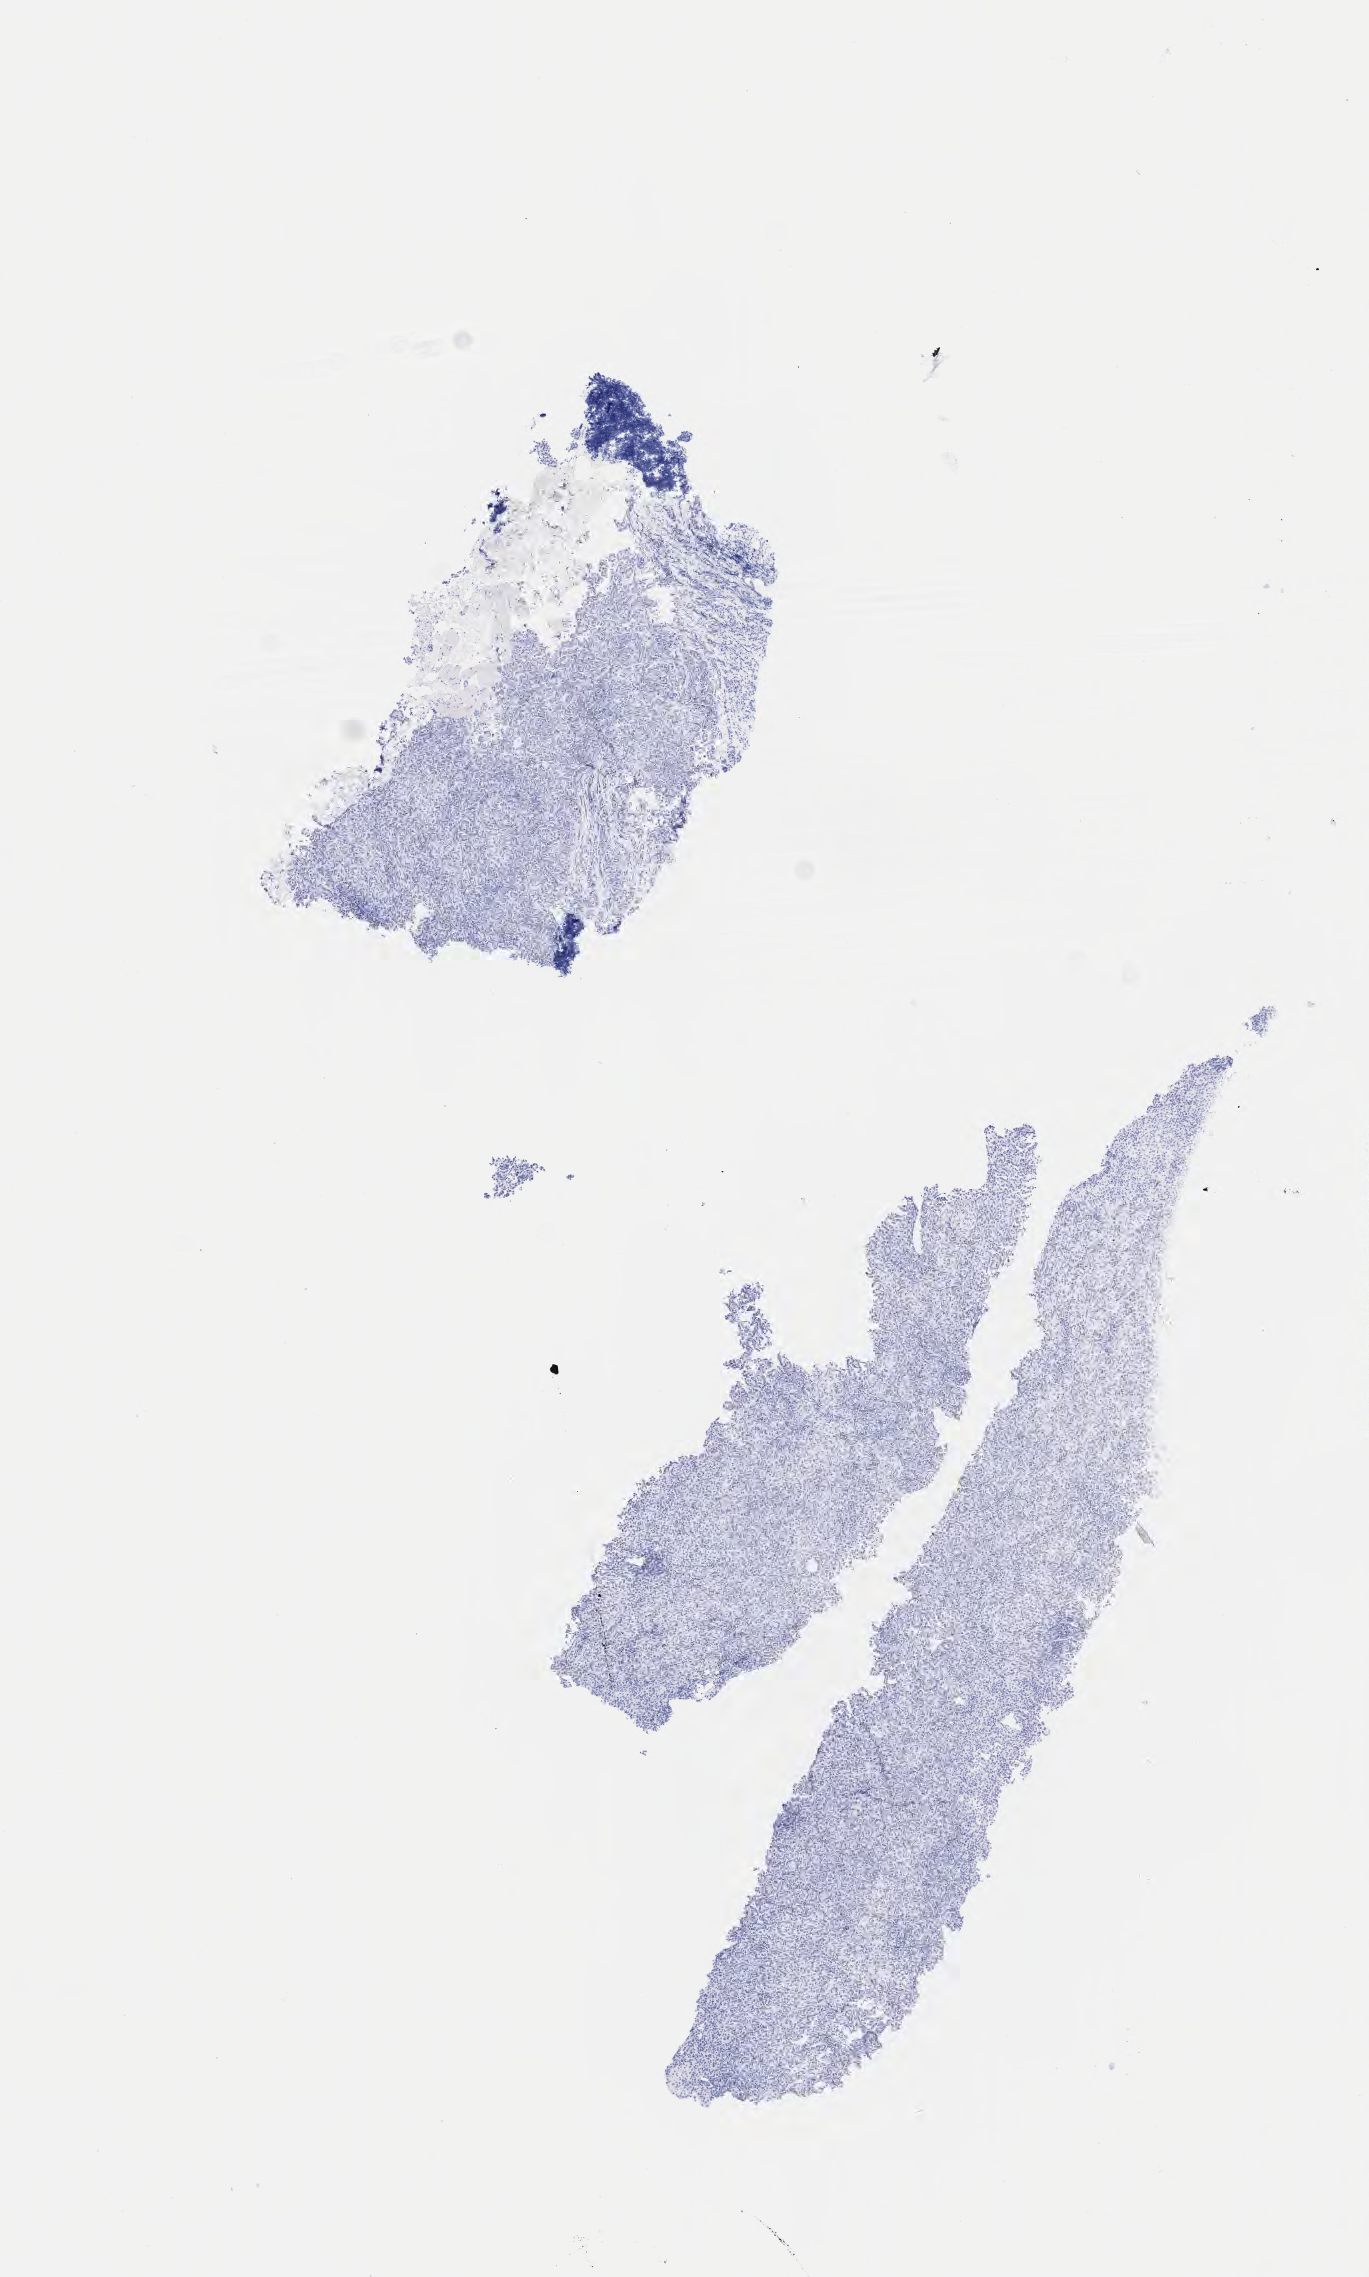
Whole-slide image, immunohistochemical stain for p40, low-resolution overview of the scanned area, about 5.5 x 9.2 mm, specimen: tumor tissue, anatomic site: lung (left). Female patient, age 65 years.
Diagnosis: Non-small cell carcinoma.